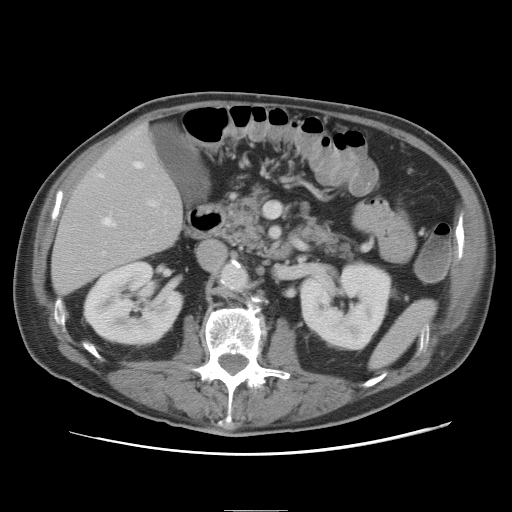
Contrast-enhanced abdominal CT, one axial slice; slice 29 of 89 in the series (ordered by position); 120 kVp; intravenous contrast given; soft-tissue window (W 400 / L 40 HU); 5 mm slice thickness; 512 × 512 image matrix. Male patient, age 69 years. From the clinical record (not read from this slice): diagnosis: colorectal cancer liver metastases, imaged before liver resection; multiple liver metastases: no; largest metastasis: 8.5 cm.
Annotated regions visible in this slice (manually delineated by an expert):
- hepatic veins: bounding box [x1, y1, x2, y2] px = [99, 161, 143, 226]
- liver: [53, 124, 182, 295]
- planned liver remnant (the part of the liver to remain after resection): [53, 124, 182, 294]
- portal vein (with intrahepatic branches): [104, 200, 158, 253]